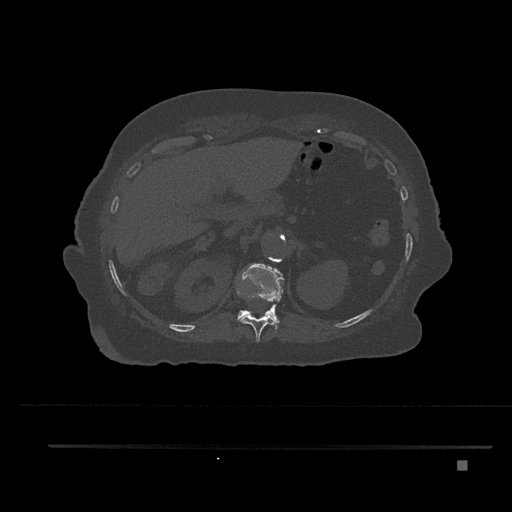
CT including the spine, one axial slice; slice 291 of 797 in the series (ordered by position); 120 kVp; bone window (W 1800 / L 400 HU); 0.5 mm slice thickness; 512 × 512 image matrix, field of view 437 × 437 mm. Patient: female, 76 years. Case-level facts recorded for this patient, not image findings: primary cancer: lung.
Annotated regions visible in this slice (semi-automatic segmentation, software-assisted and operator-edited):
- T11 vertebra: bounding box <236,290,278,342> (left, top, right, bottom; pixels)
- T12 vertebra: <236,264,284,329>